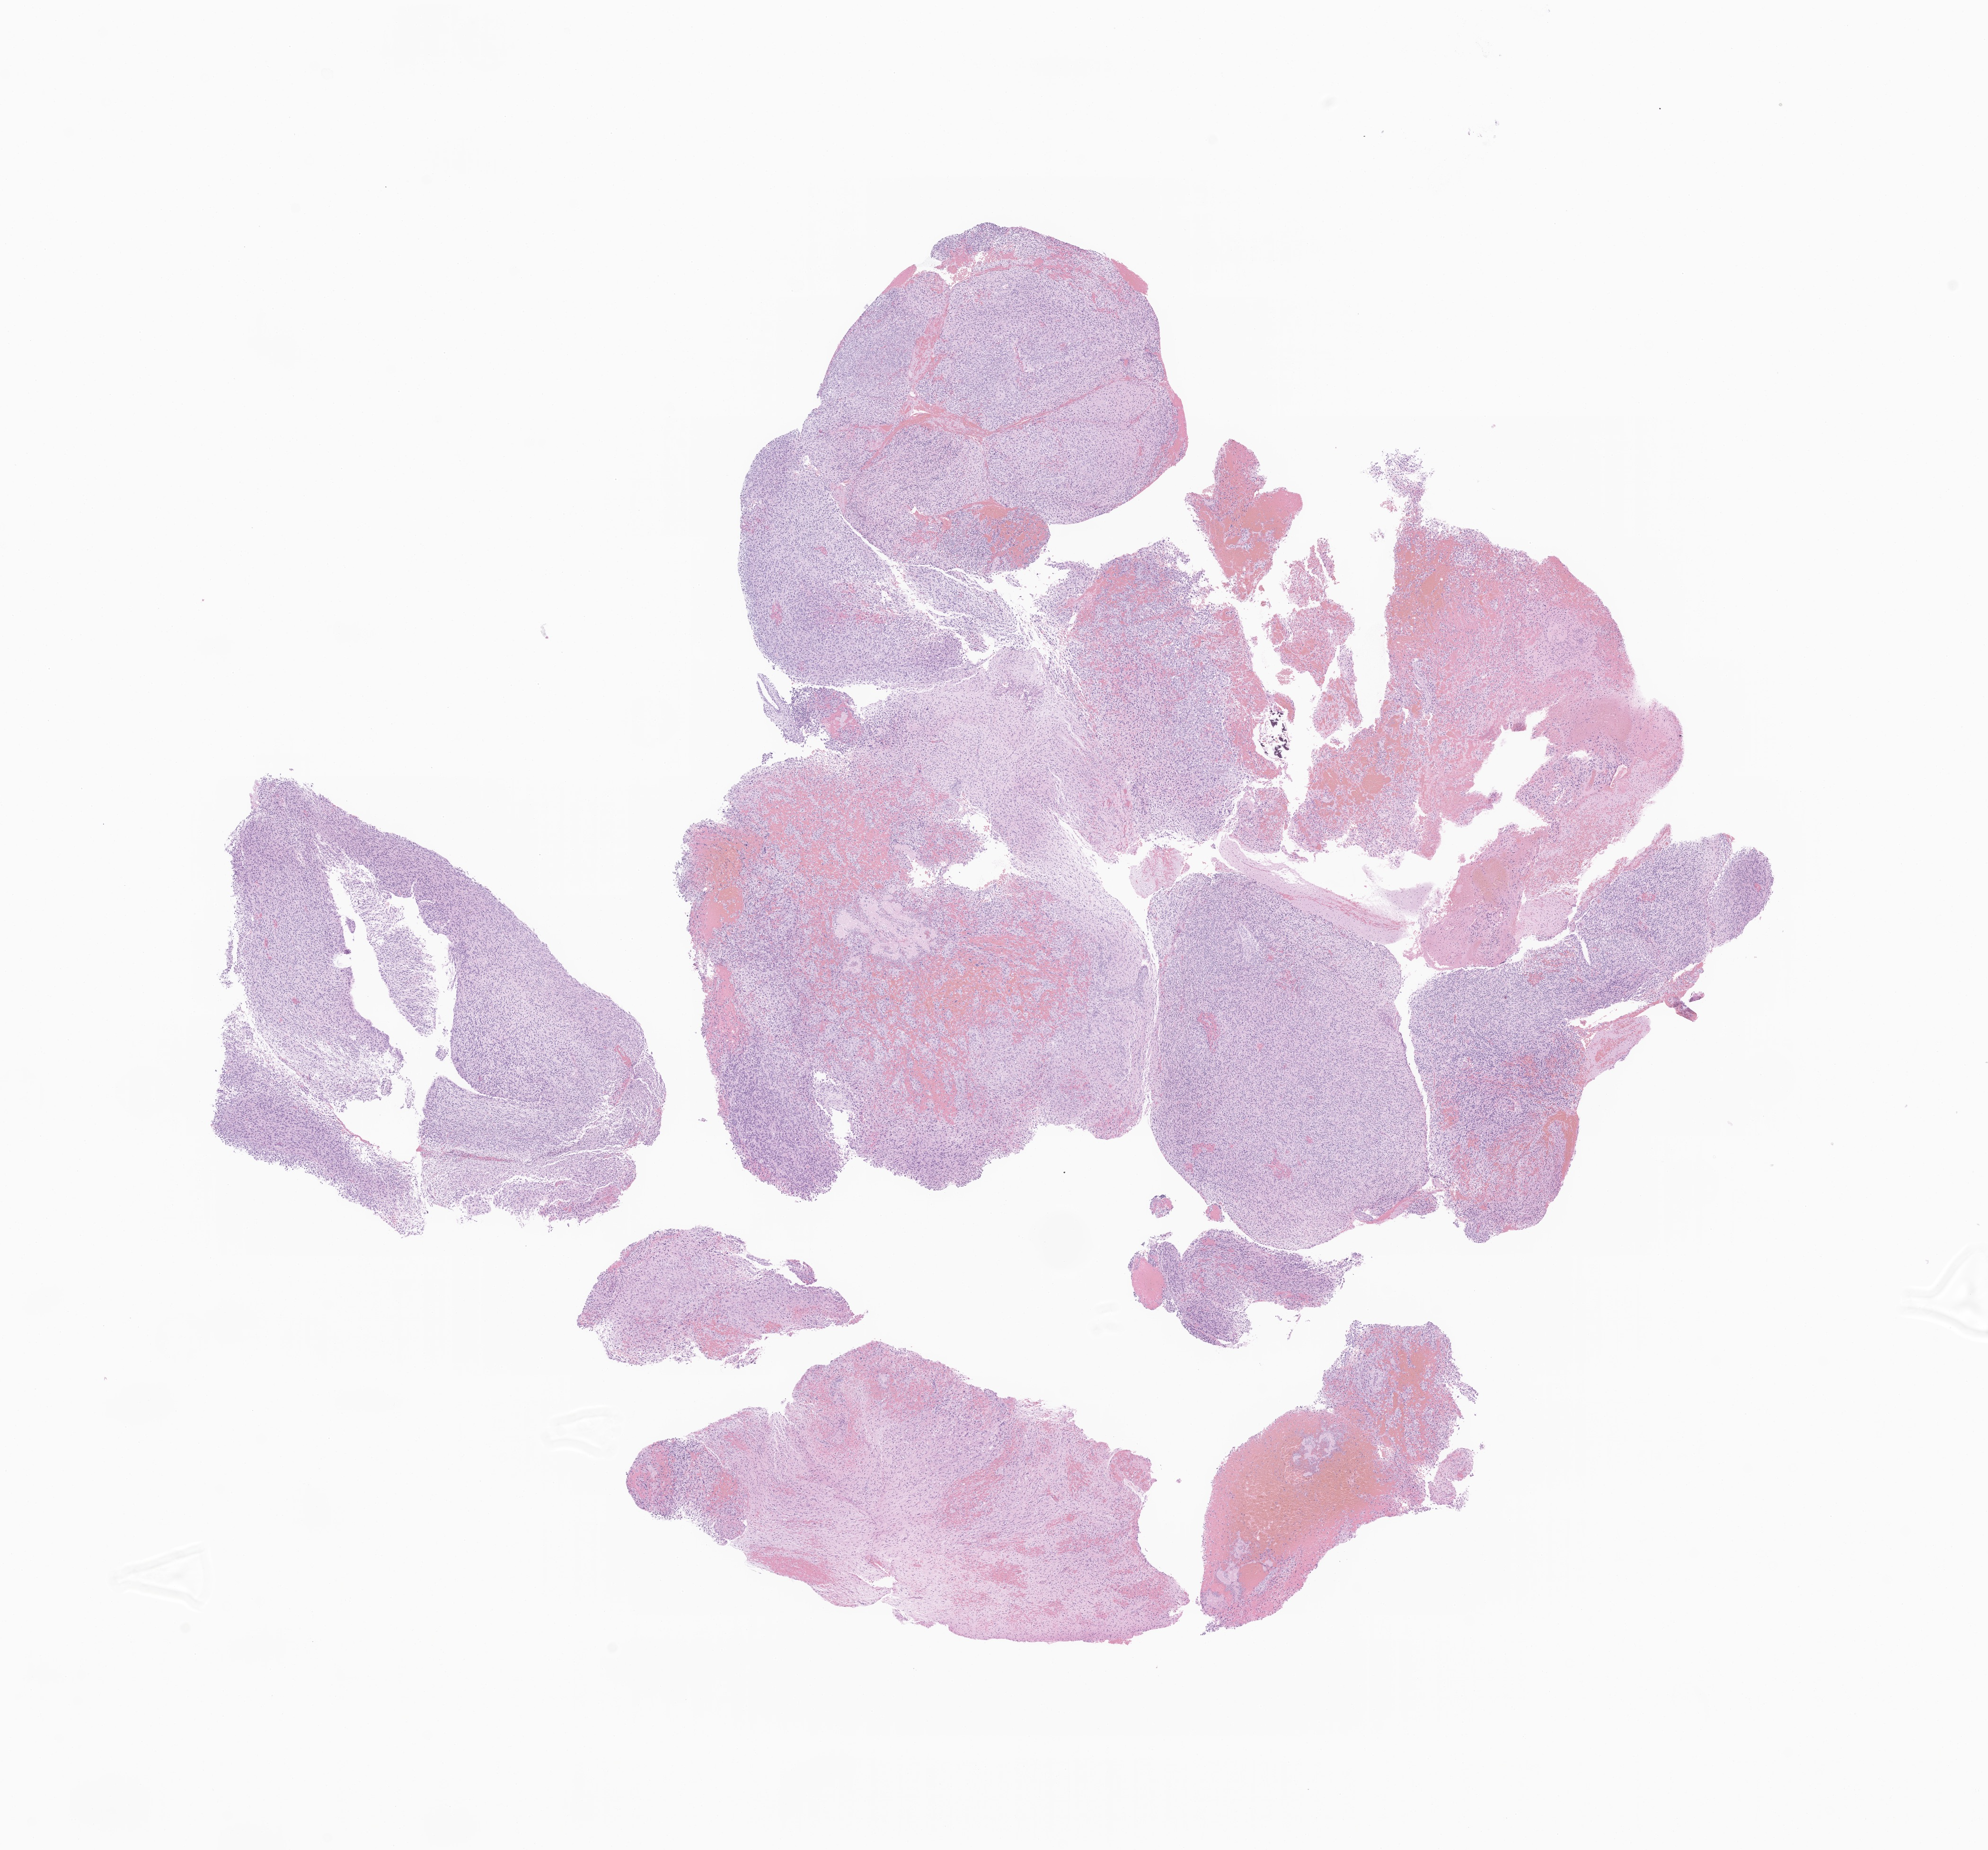
Digitized hematoxylin and eosin (H&E)-stained section of tumor tissue from the brain, shown as a low-resolution overview of the whole scanned area (about 17.7 x 16.5 mm); formalin-fixed paraffin-embedded section. Patient female; age 202 months (16 years 10 months).
Diagnosis (ICD-O-3 morphology term): Glioma, malignant.